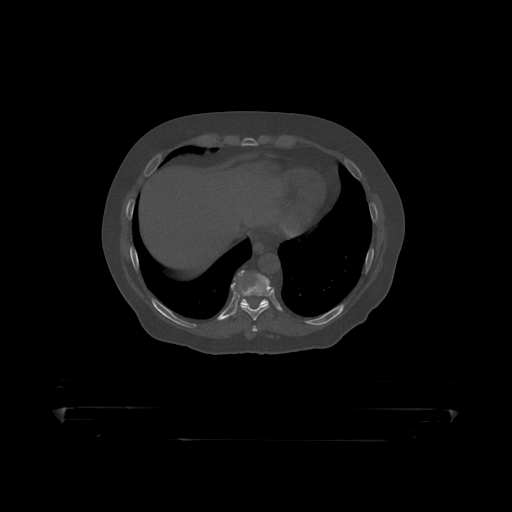
CT including the spine, one axial slice. Slice 231 of 390 in the series (ordered by position). Reconstruction kernel STANDARD. Bone window (W 1800 / L 400 HU). 1.25 mm slice thickness. 512 × 512 image matrix, field of view 650 × 650 mm. Male patient, age 60 years. Case-level facts recorded for this patient, not image findings: primary cancer: prostate.
Structures marked on this image (semi-automatically segmented with operator editing):
- T10 vertebra: bounding box <240,299,267,306> (left, top, right, bottom; pixels)
- T9 vertebra: <231,270,272,319>